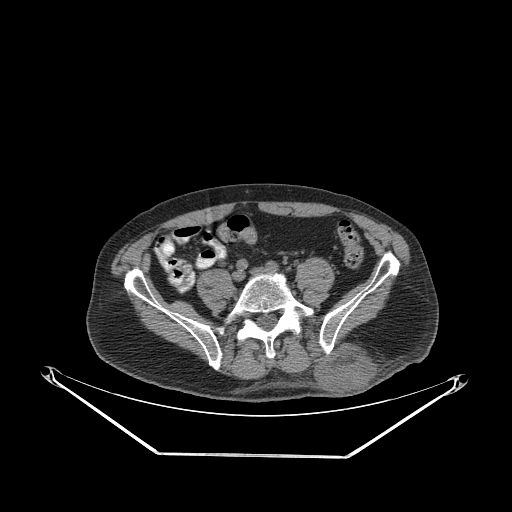
CT of an extremity soft-tissue mass (from a PET/CT study), one axial slice; position 86 of 267 along the scan axis; reconstruction kernel STANDARD; soft-tissue window (W 400 / L 40 HU); 3.75 mm slice thickness; 512 × 512 image matrix. Male patient. From the clinical record (not read from this slice): histological type: leiomyosarcoma; grade: intermediate; site of the primary tumour: left pelvis.
Outlined on this slice (expert contour drawn on MRI and transferred to this co-registered scan by the dataset authors):
- gross tumour volume (mass): bounding box [x1, y1, x2, y2] px = [313, 342, 378, 394]